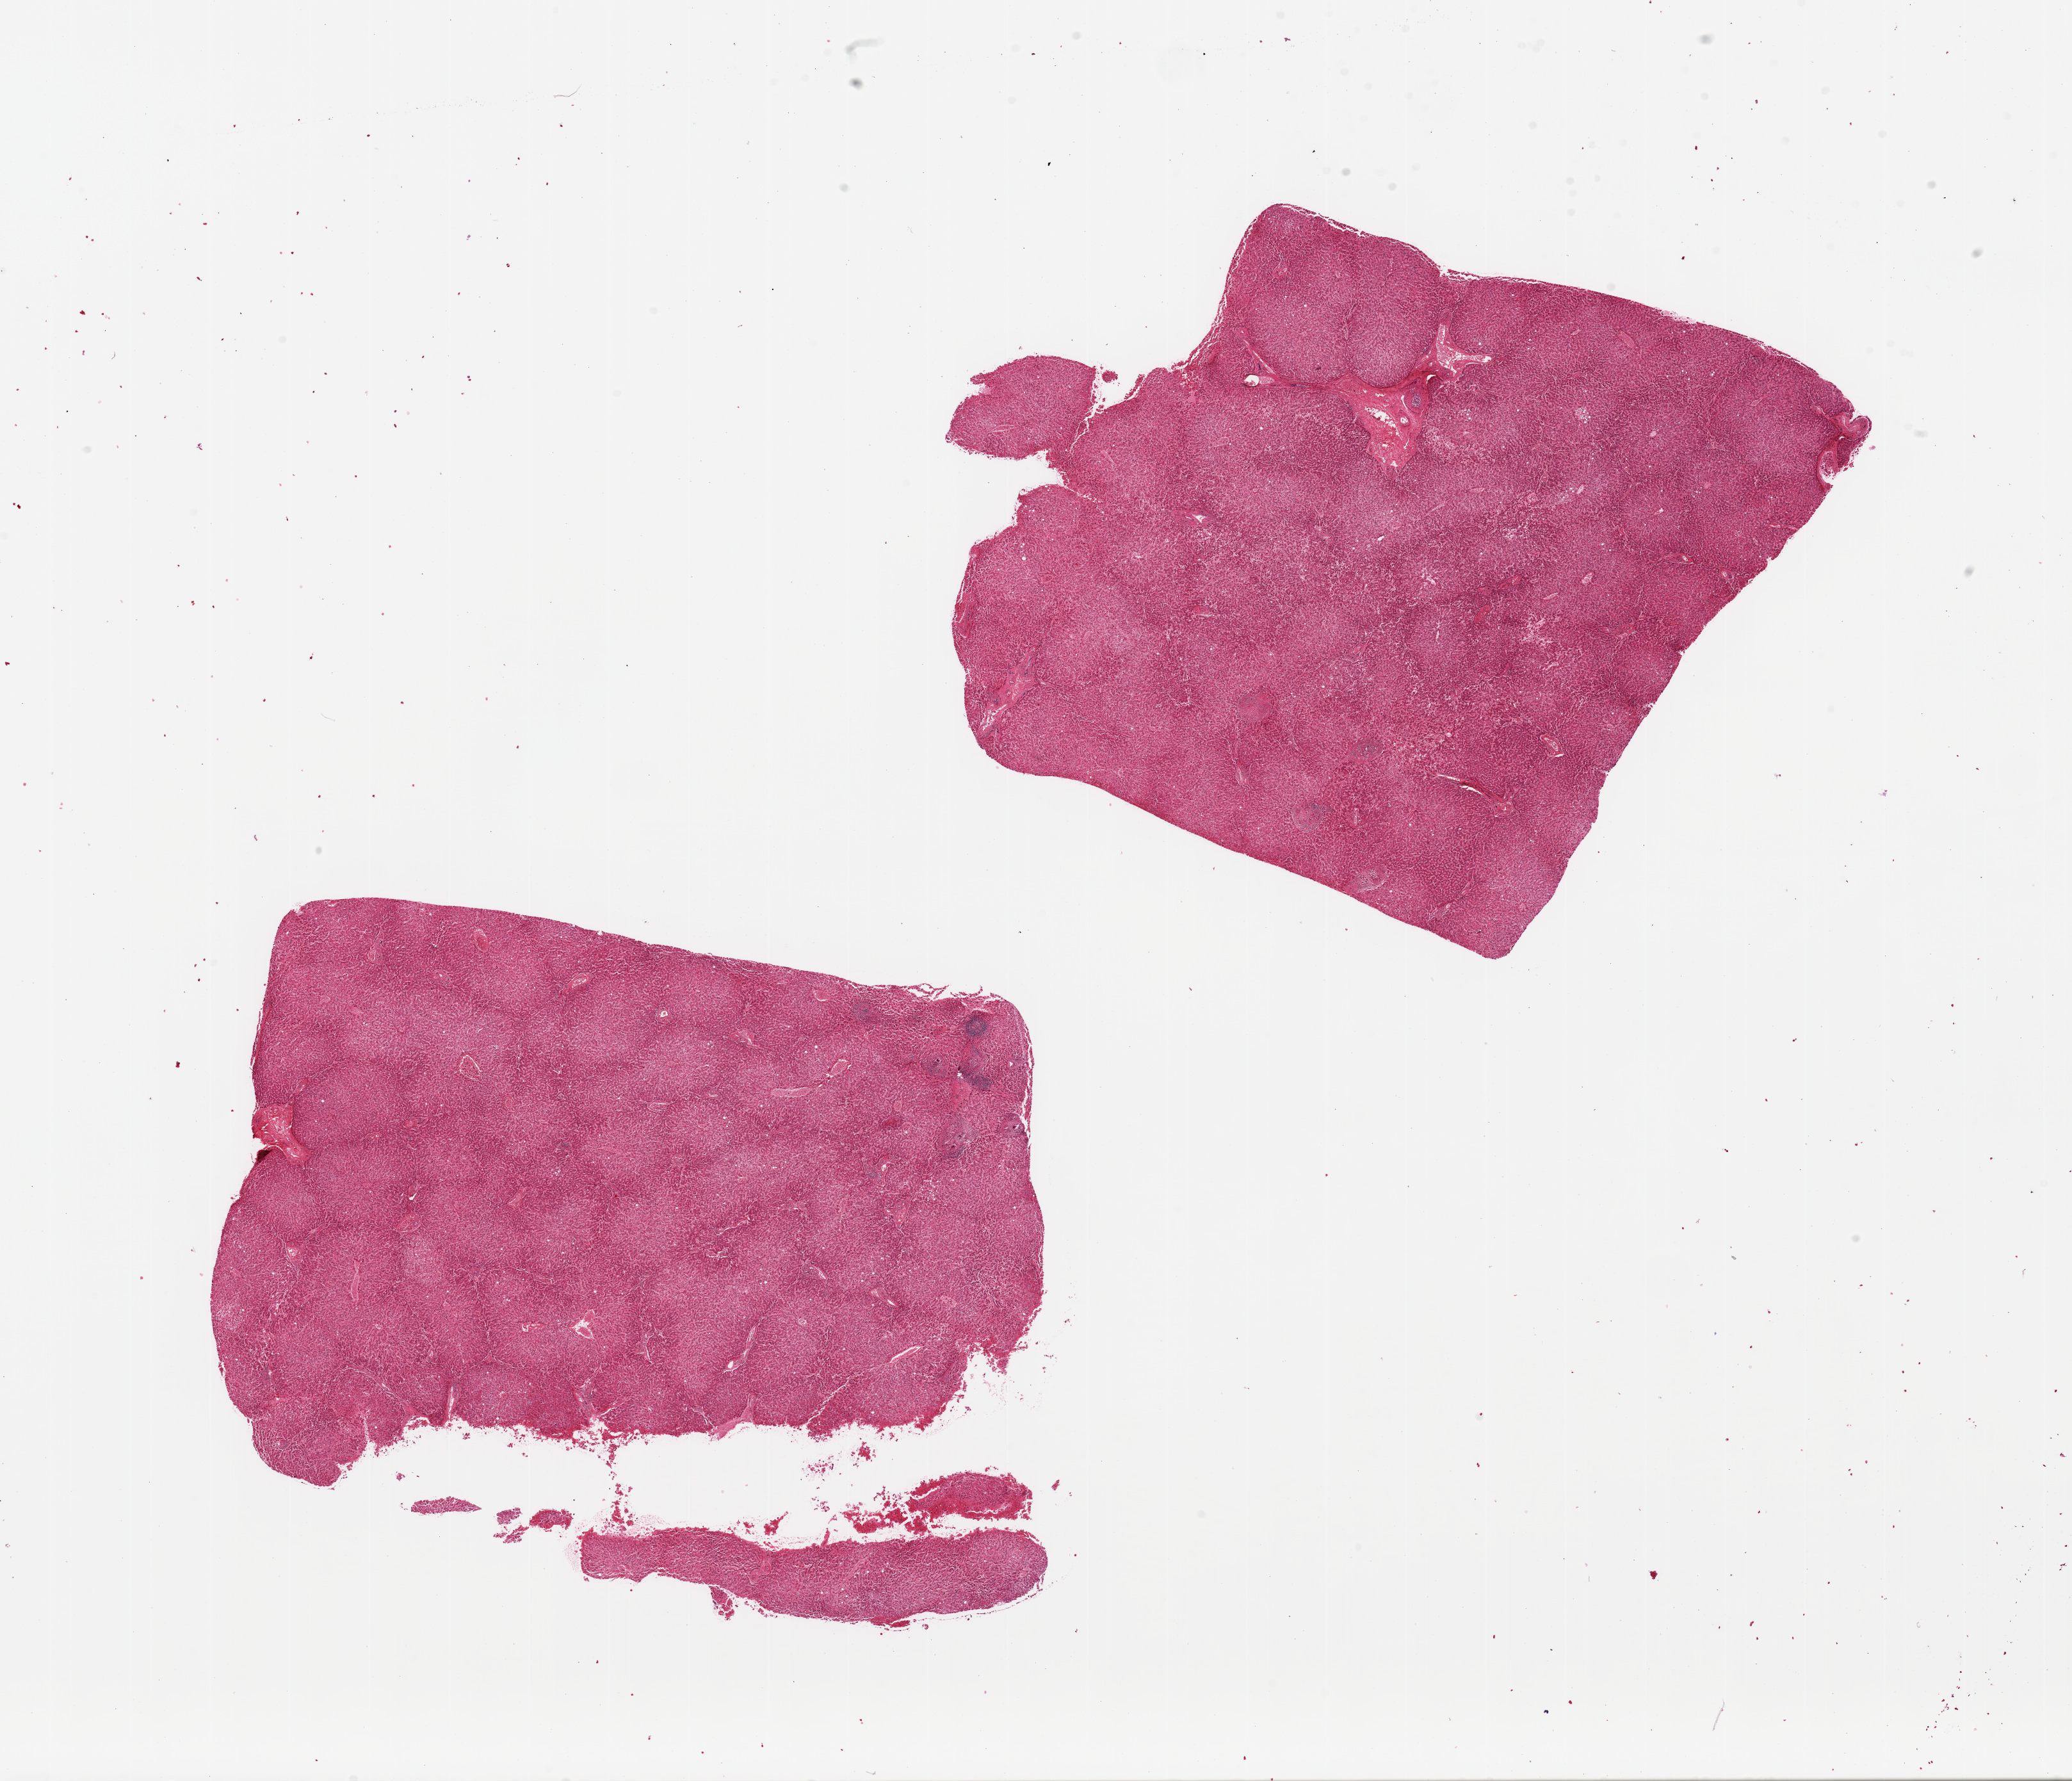
Hematoxylin and eosin (H&E) whole-slide image, low-resolution overview of the scanned area, about 25.6 x 22.0 mm; PAXgene-fixed paraffin-embedded (PFPE) section; section of liver (target tissue); donor tissue sample.
* review note (as recorded): 2 pieces, diffuse microvesicular steatosis, granulomas noted